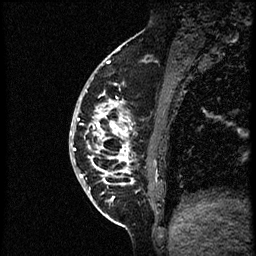
Breast MRI (dynamic contrast-enhanced), one sagittal slice; slice 20 of 56 in the series (ordered by position); dynamic contrast-enhanced study with each time point stored as its own series, time point 2 of 3 at this slice position (early post-contrast, ordered by acquisition time); 1.5 T; TE 4.2 ms, TR 21.3 ms; 2 mm slice thickness; 256 × 256 image matrix, field of view 200 × 200 mm. Female patient, age 41 years. Case-level facts recorded for this patient, not image findings: setting: breast cancer imaged before/during neoadjuvant chemotherapy; receptor status: HER2-positive.
Outlined on this slice (semi-automatic segmentation, software-assisted and operator-edited):
- analysis volume of interest (the breast-tissue region the enhancement analysis was run in; not a lesion): bounding box (x1, y1, x2, y2) in pixels: (70, 73, 169, 205)
- tumour enhancement mask (voxels above the 100 % enhancement threshold inside the analysis volume of interest): (72, 86, 134, 200)